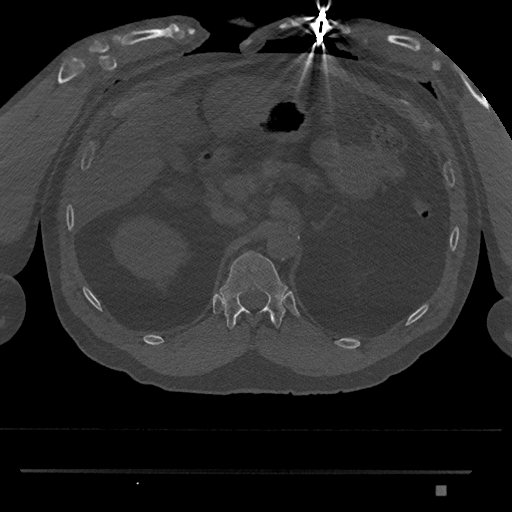
CT including the spine, one axial slice; position 900 of 1134 along the scan axis; reconstruction kernel Br40s/3; bone window (W 1800 / L 400 HU); 0.5 mm slice thickness; 512 × 512 image matrix, field of view 429 × 429 mm. Male patient, age 65 years. From the clinical record (not read from this slice): primary cancer: prostate.
Structures marked on this image (semi-automatic segmentation, software-assisted and operator-edited):
- T11 vertebra: bounding box [x1, y1, x2, y2] px = [250, 346, 252, 348]
- T12 vertebra: [219, 250, 288, 330]